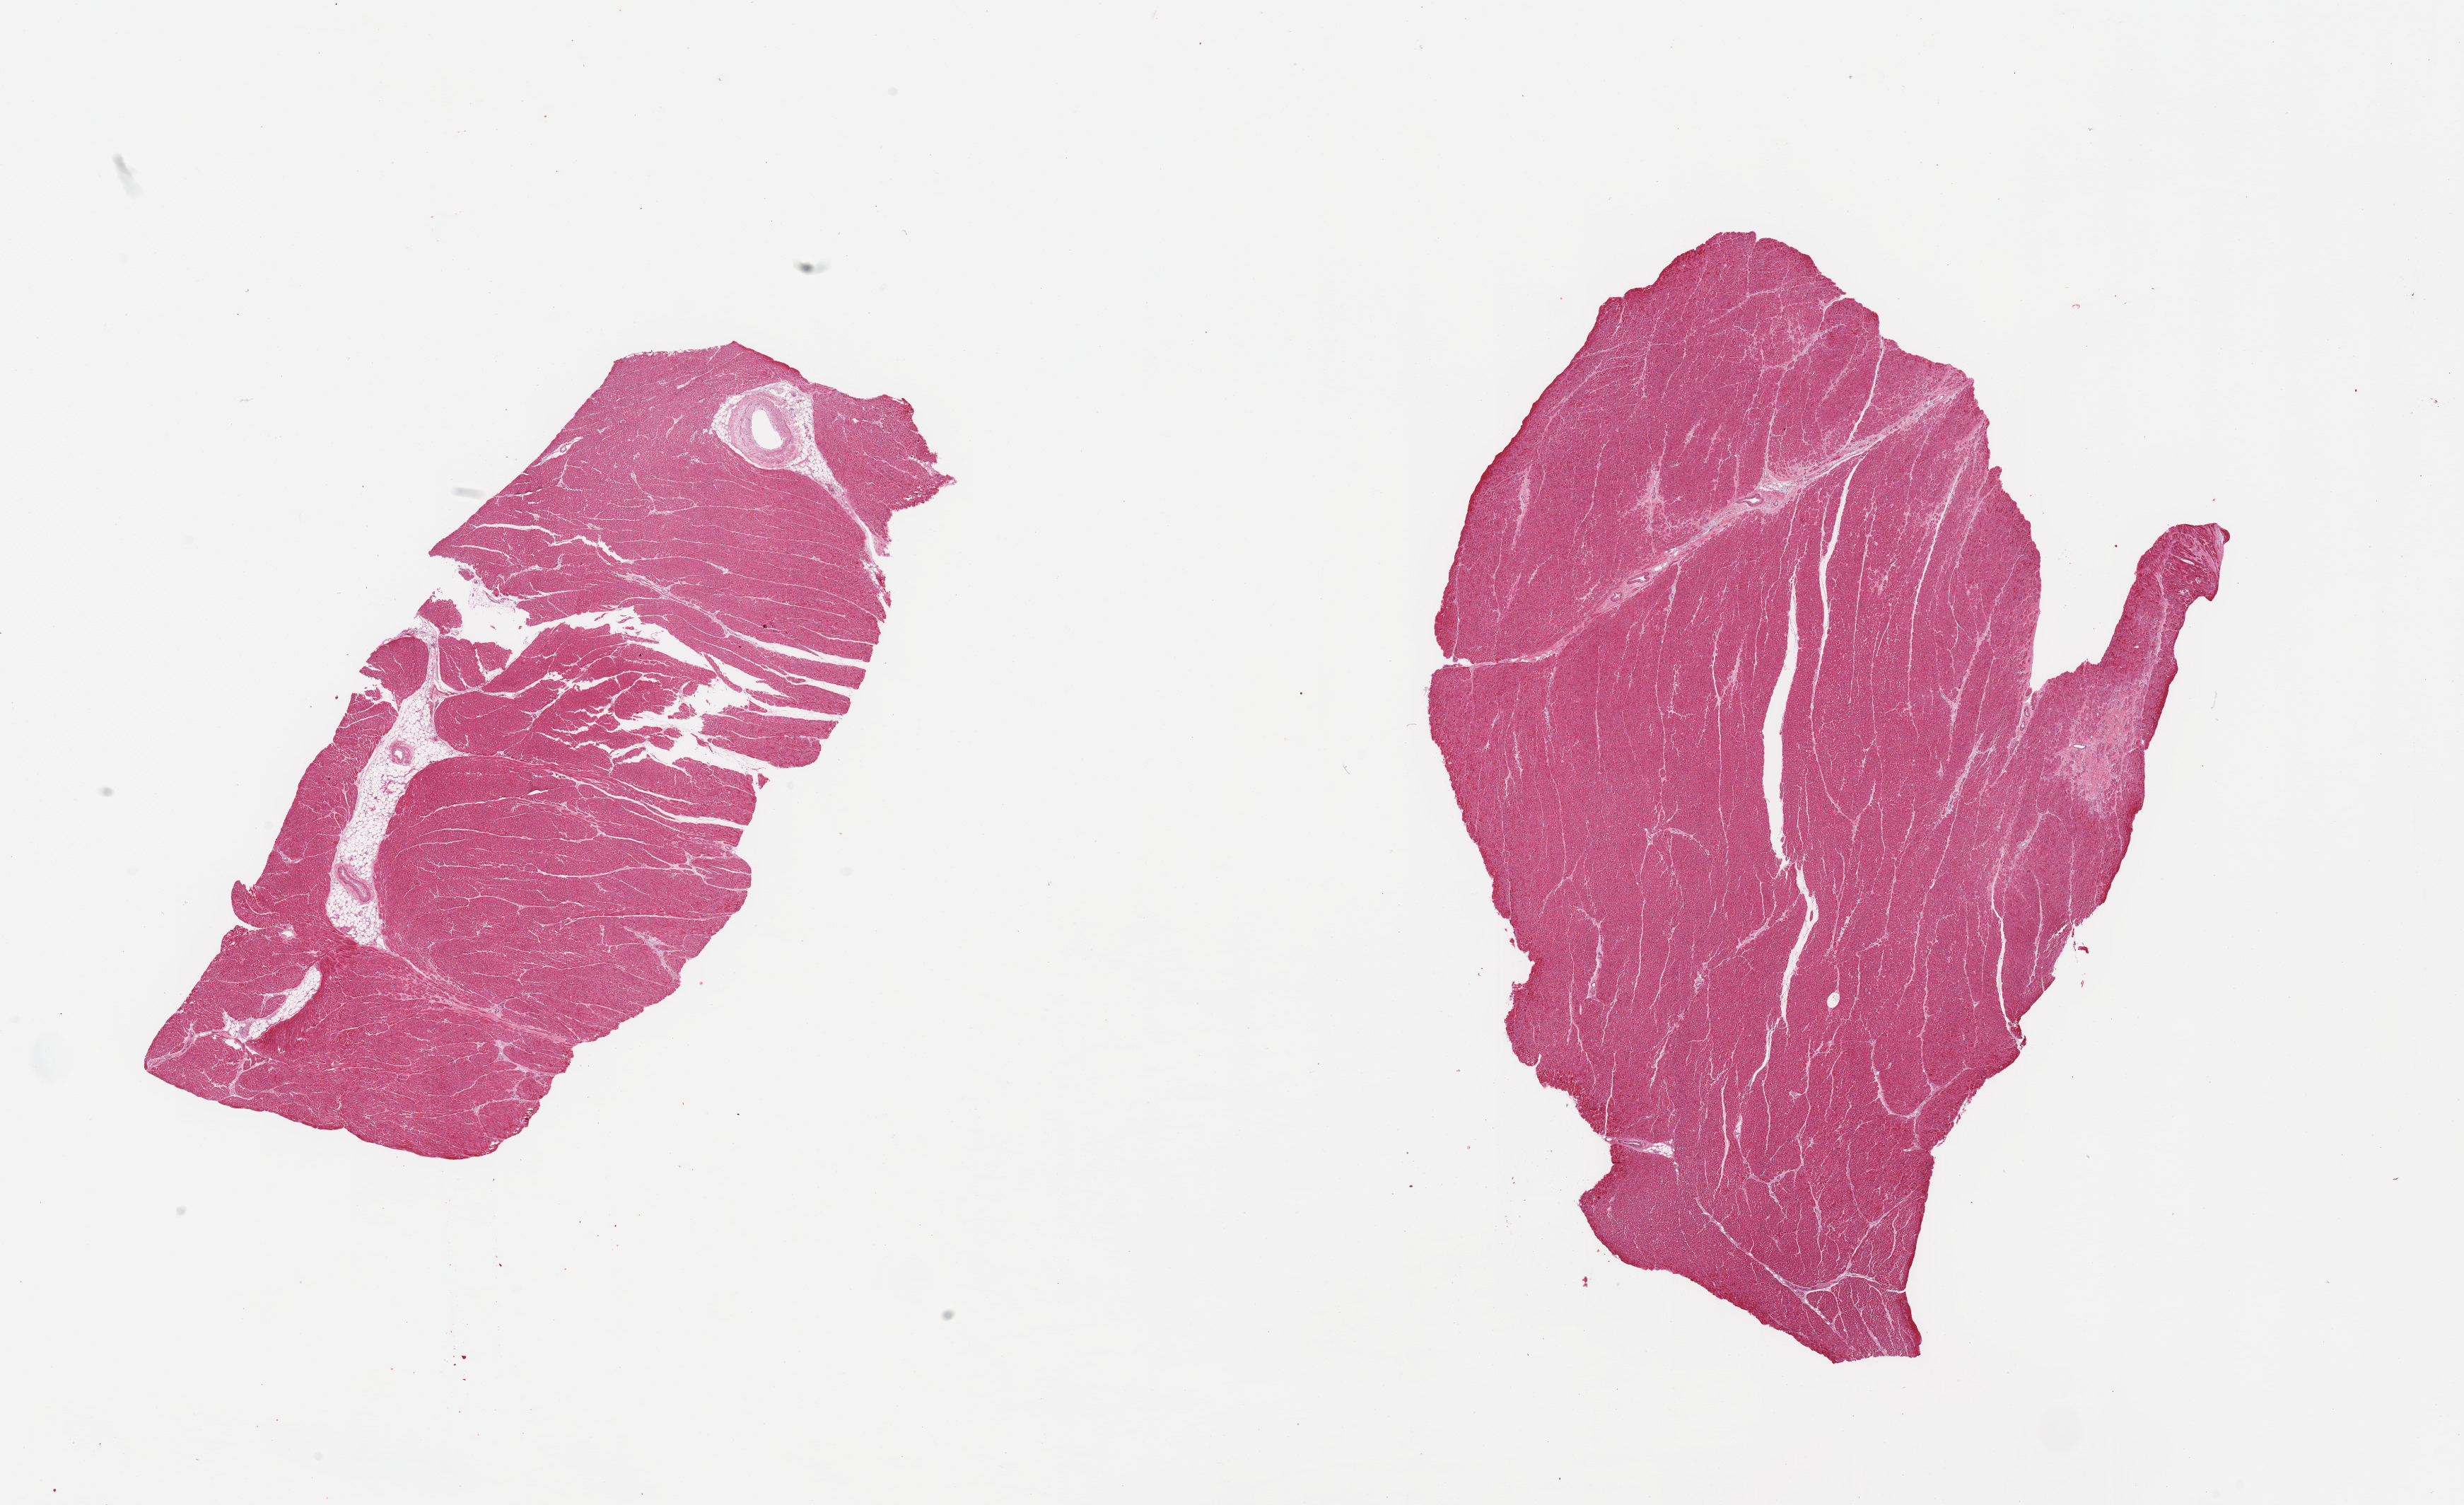
H&E whole-slide image, shown as a low-resolution overview of the whole scanned area (about 27.6 x 16.8 mm, from a 20x scan). PAXgene-fixed paraffin-embedded (PFPE) section. Target tissue: heart. Tissue donor sample. Donor sex: male.
Pathologist's review note for this sample: 2 pieces, moderate chronic ischemic changes/interstitial fibrosis; ~2mm remote micro-infarct.